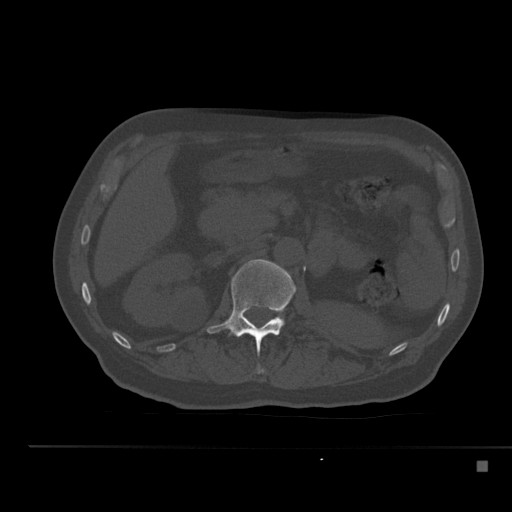
CT including the spine, one axial slice. Slice 207 of 517 in the series (ordered by position). Bone window (W 1800 / L 400 HU). 1.5 mm slice thickness. 512 × 512 image matrix, field of view 408 × 408 mm. Patient: male, 70 years. From the clinical record (not read from this slice): primary cancer: renal.
Structures marked on this image (semi-automatic segmentation, software-assisted and operator-edited):
- L1 vertebra: bounding box [x1, y1, x2, y2] px = [206, 259, 296, 355]
- T12 vertebra: [257, 365, 264, 374]